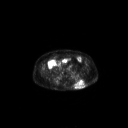
FDG PET of an extremity soft-tissue mass (from a PET/CT study), one axial slice; slice 80 of 267 in the series (ordered by position); 128 × 128 image matrix. Male patient, age 69 years. Case-level facts recorded for this patient, not image findings: histological type: leiomyosarcoma; grade: intermediate; site of the primary tumour: left pelvis.
Structures marked on this image (expert contour drawn on MRI and transferred to this co-registered scan by the dataset authors):
- gross tumour volume (mass): box from (x=73, y=79) to (x=85, y=89) px